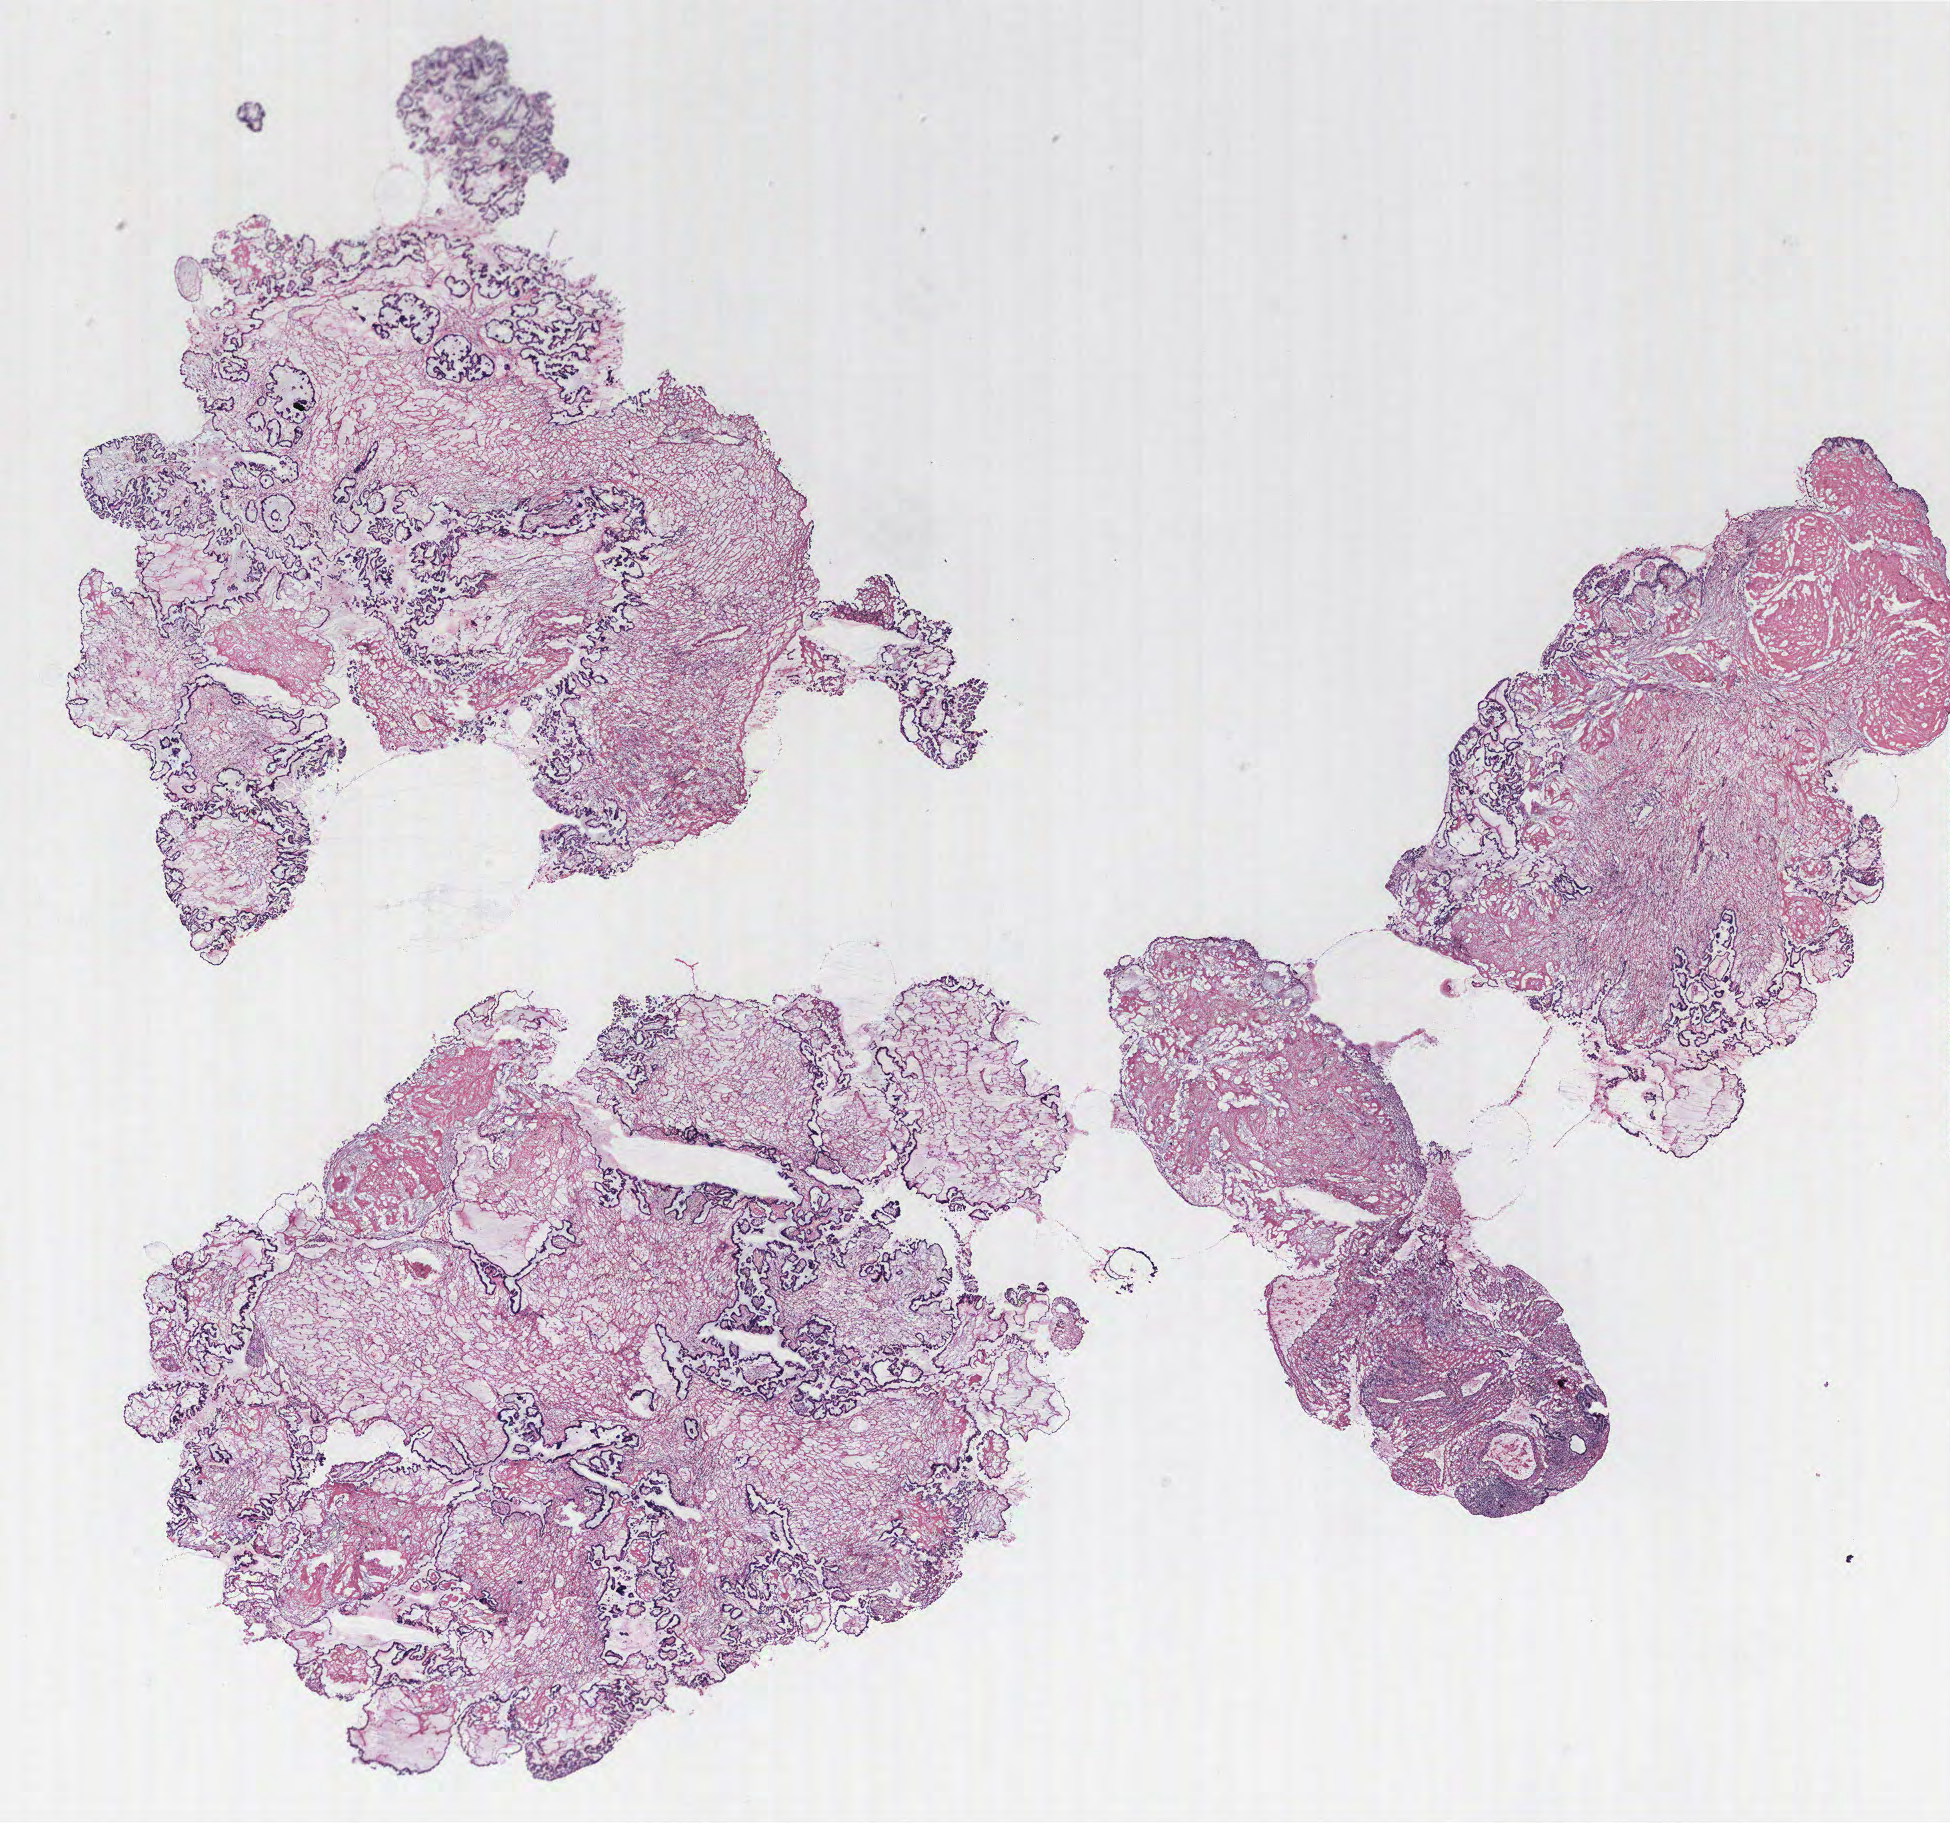
Whole-slide histology image, Hematoxylin and eosin (H&E) stained, low-resolution overview of the scanned area, about 15.6 x 14.6 mm (from a 40x scan). Ovary, tumour tissue. 49-year-old female patient.
Diagnosis: Serous adenocarcinoma, NOS. Primary tumour site (as recorded): ovary.